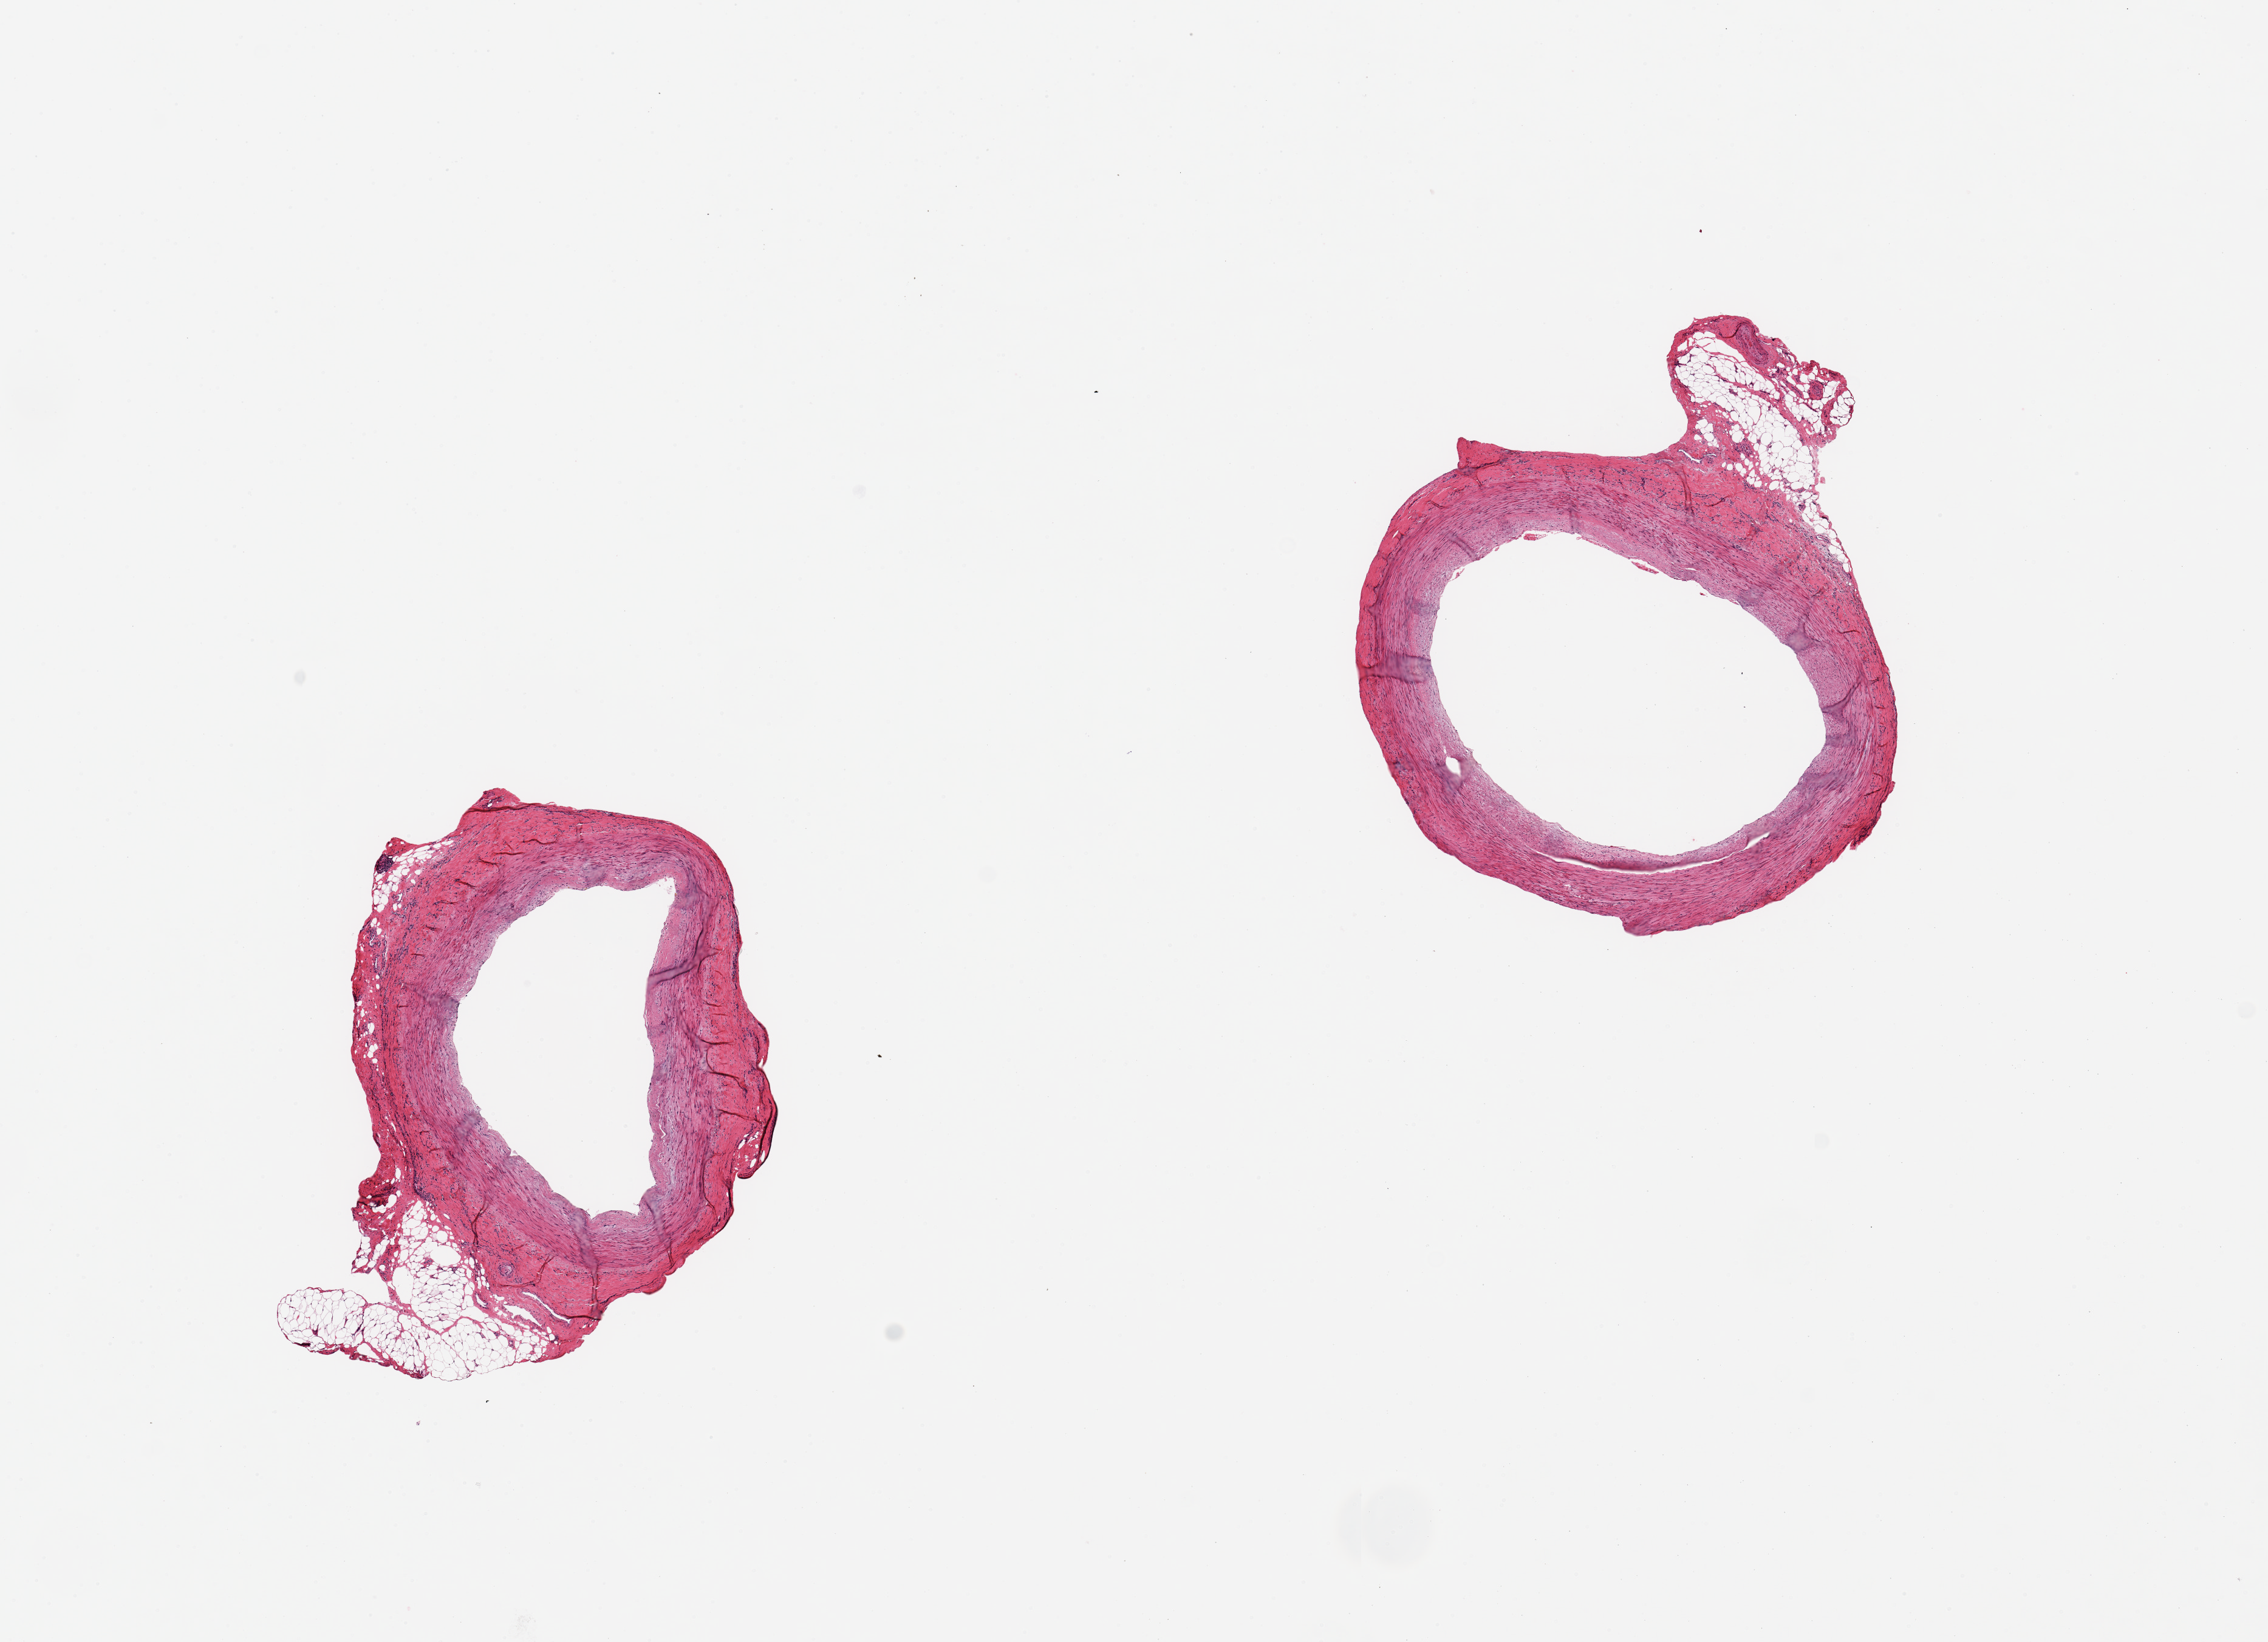
Digitized haematoxylin and eosin-stained section, whole scanned area (about 14.8 x 10.7 mm) shown as a low-resolution overview; PAXgene-fixed, paraffin-embedded tissue; section of tibial artery (target tissue); tissue donor sample.
• review note (as recorded): 2 pieces, 4x3.5 & 4x4mm; small foci of peripheral adipose